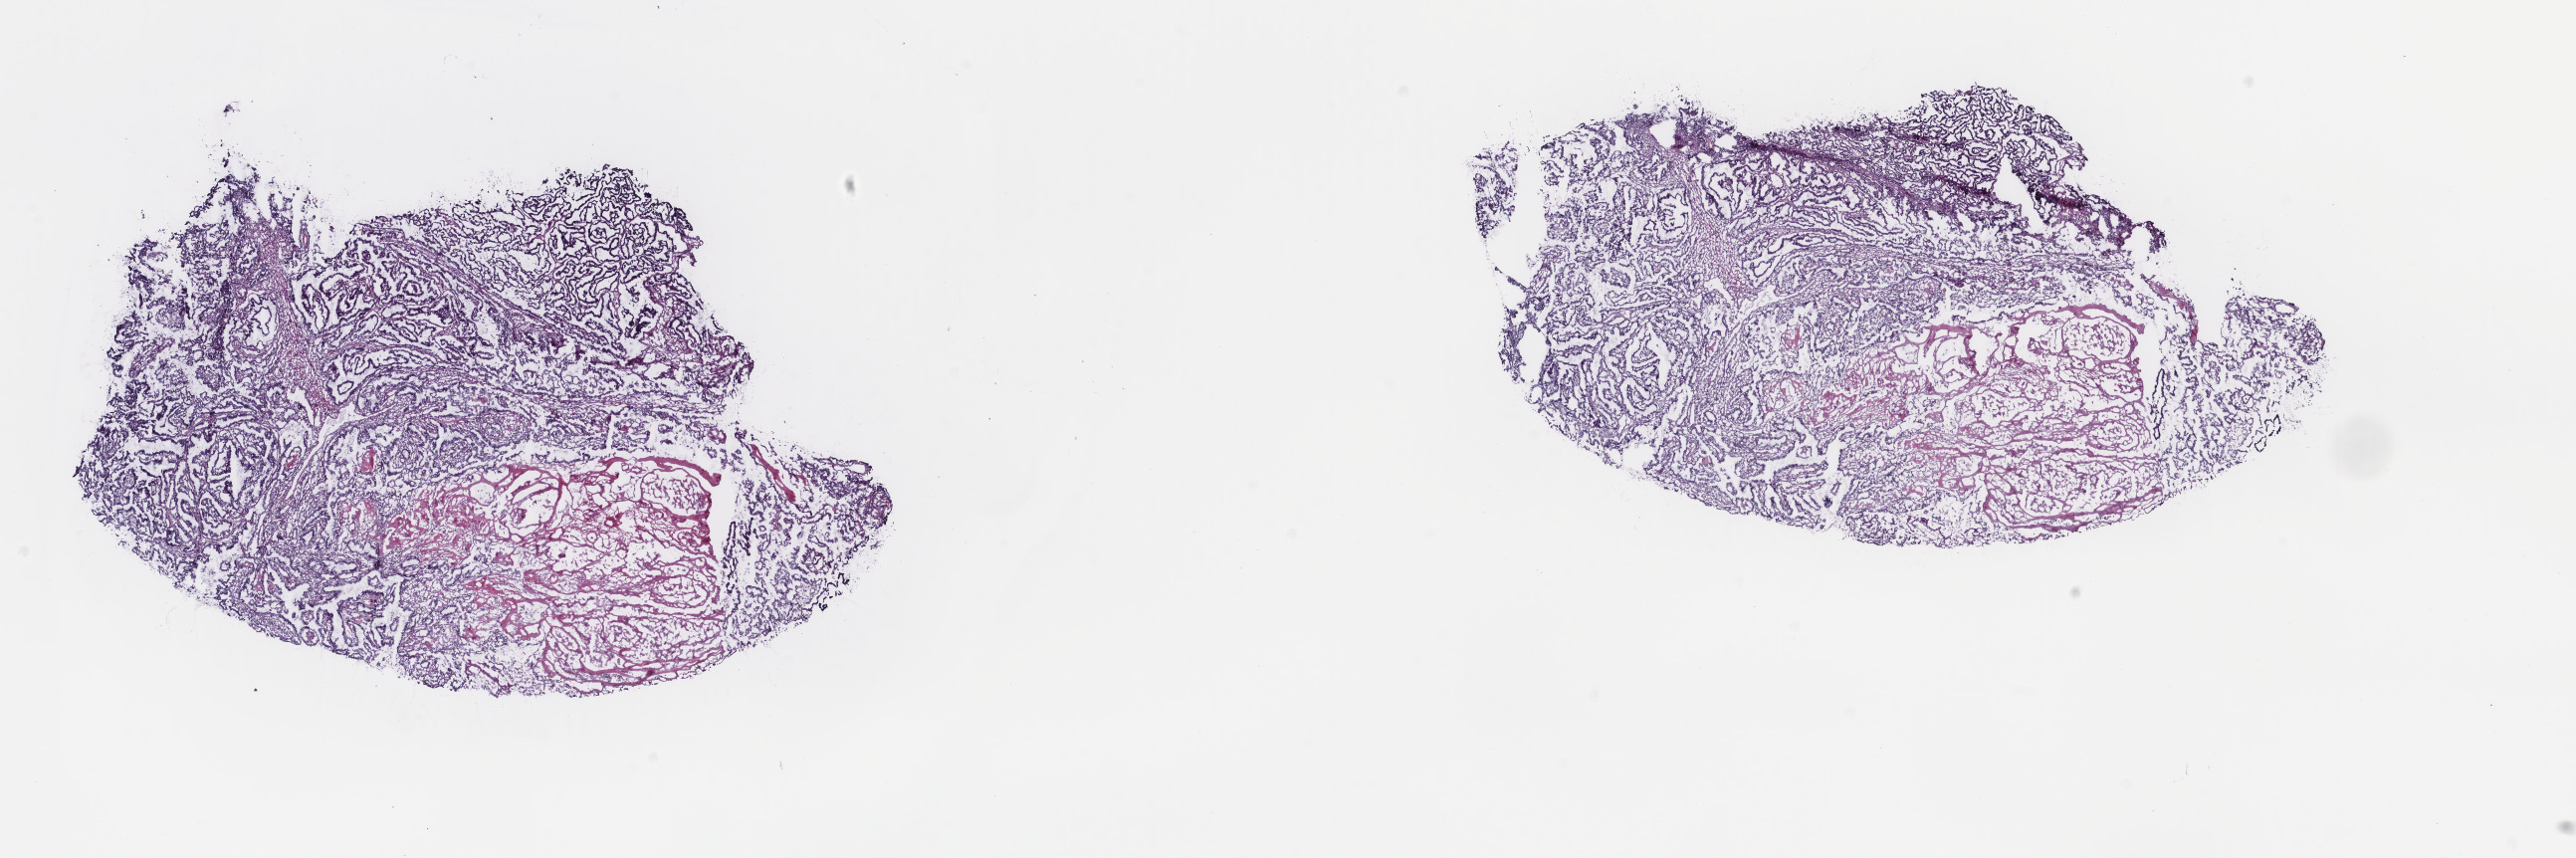
H&E whole-slide image, low-resolution overview of the scanned area, about 20.5 x 6.8 mm; frozen section from the top of the tissue portion; sample: primary tumour, uterus. Patient: female, age at initial diagnosis 68 years. Histologic grade: G1 (well differentiated). Slide review estimates, as recorded: tumour cells 60%, tumour nuclei 60%, normal cells 0%, stromal cells 30%, necrosis 10%. Infiltration values recorded for this section: lymphocyte infiltration 40%, monocyte infiltration 20%, neutrophil infiltration 20%.
FIGO stage: IIIA. Histologic diagnosis: Endometrioid adenocarcinoma, NOS (endometrium).